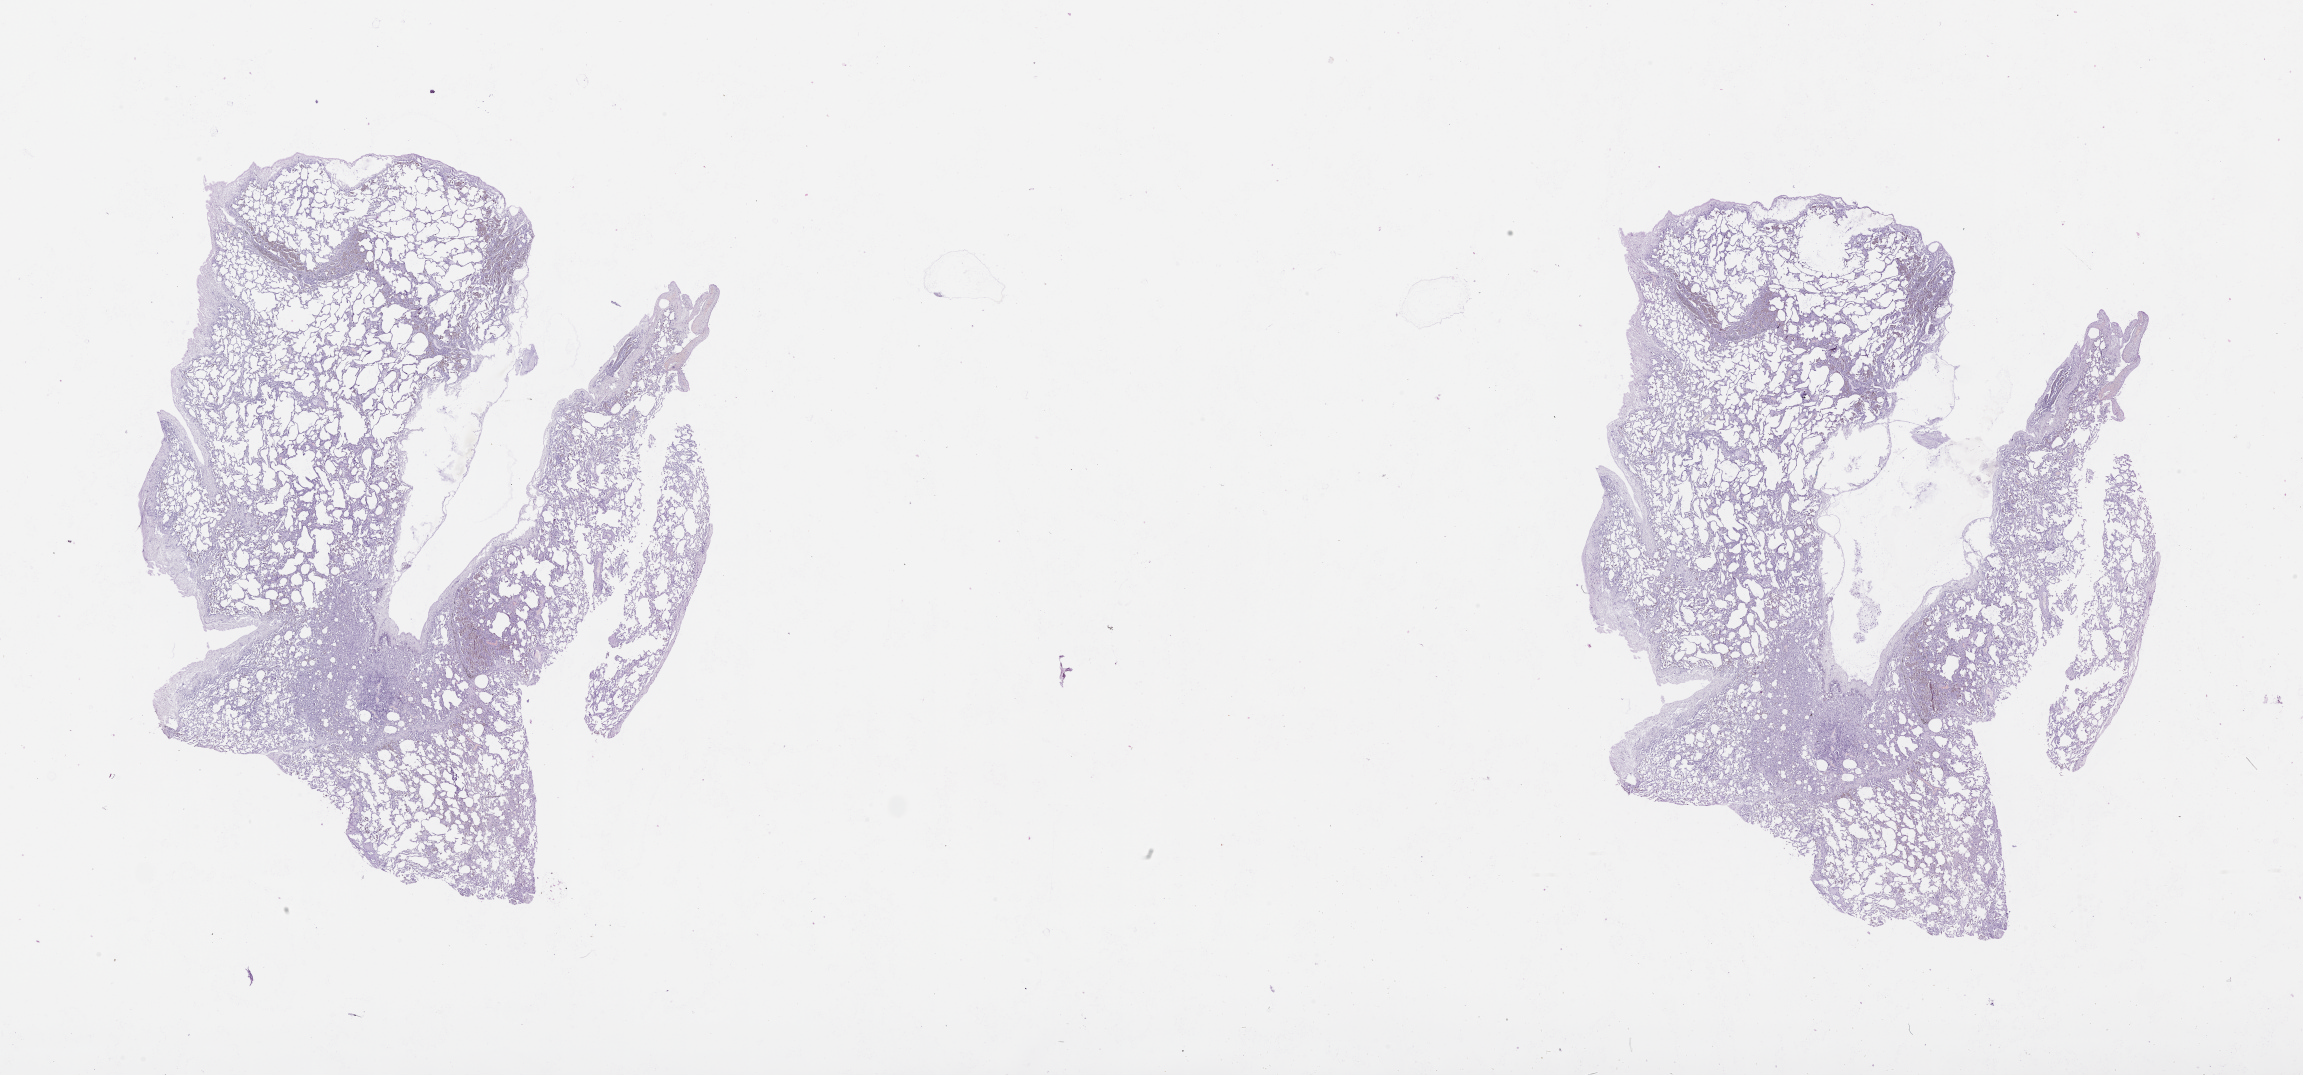
Digitized H&E tissue section (whole slide), whole scanned area (about 37.1 x 17.3 mm, acquisition: 20x scan) shown as a low-resolution overview. Lung, tissue type not recorded.
* patient diagnosis (cohort enrolment): lung adenocarcinoma (lung)